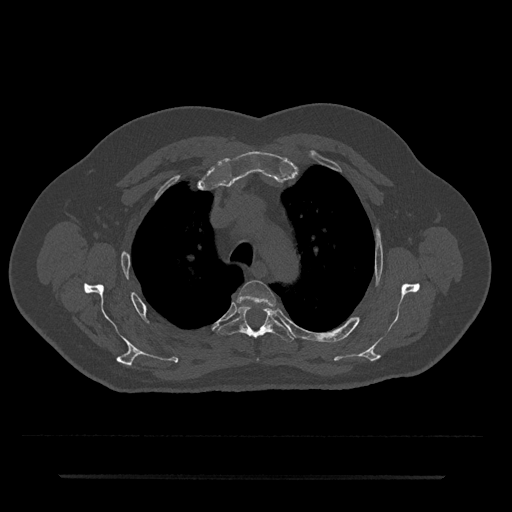
CT including the spine, one axial slice. Position 541 of 797 along the scan axis. 120 kVp. Bone window (W 1800 / L 400 HU). 0.5 mm slice thickness. 512 × 512 image matrix. Patient: male, 69 years. From the clinical record (not read from this slice): primary cancer: prostate.
Outlined on this slice (semi-automatic segmentation, software-assisted and operator-edited):
- T3 vertebra: bounding box [x1, y1, x2, y2] px = [238, 280, 276, 306]
- T4 vertebra: [217, 305, 294, 342]